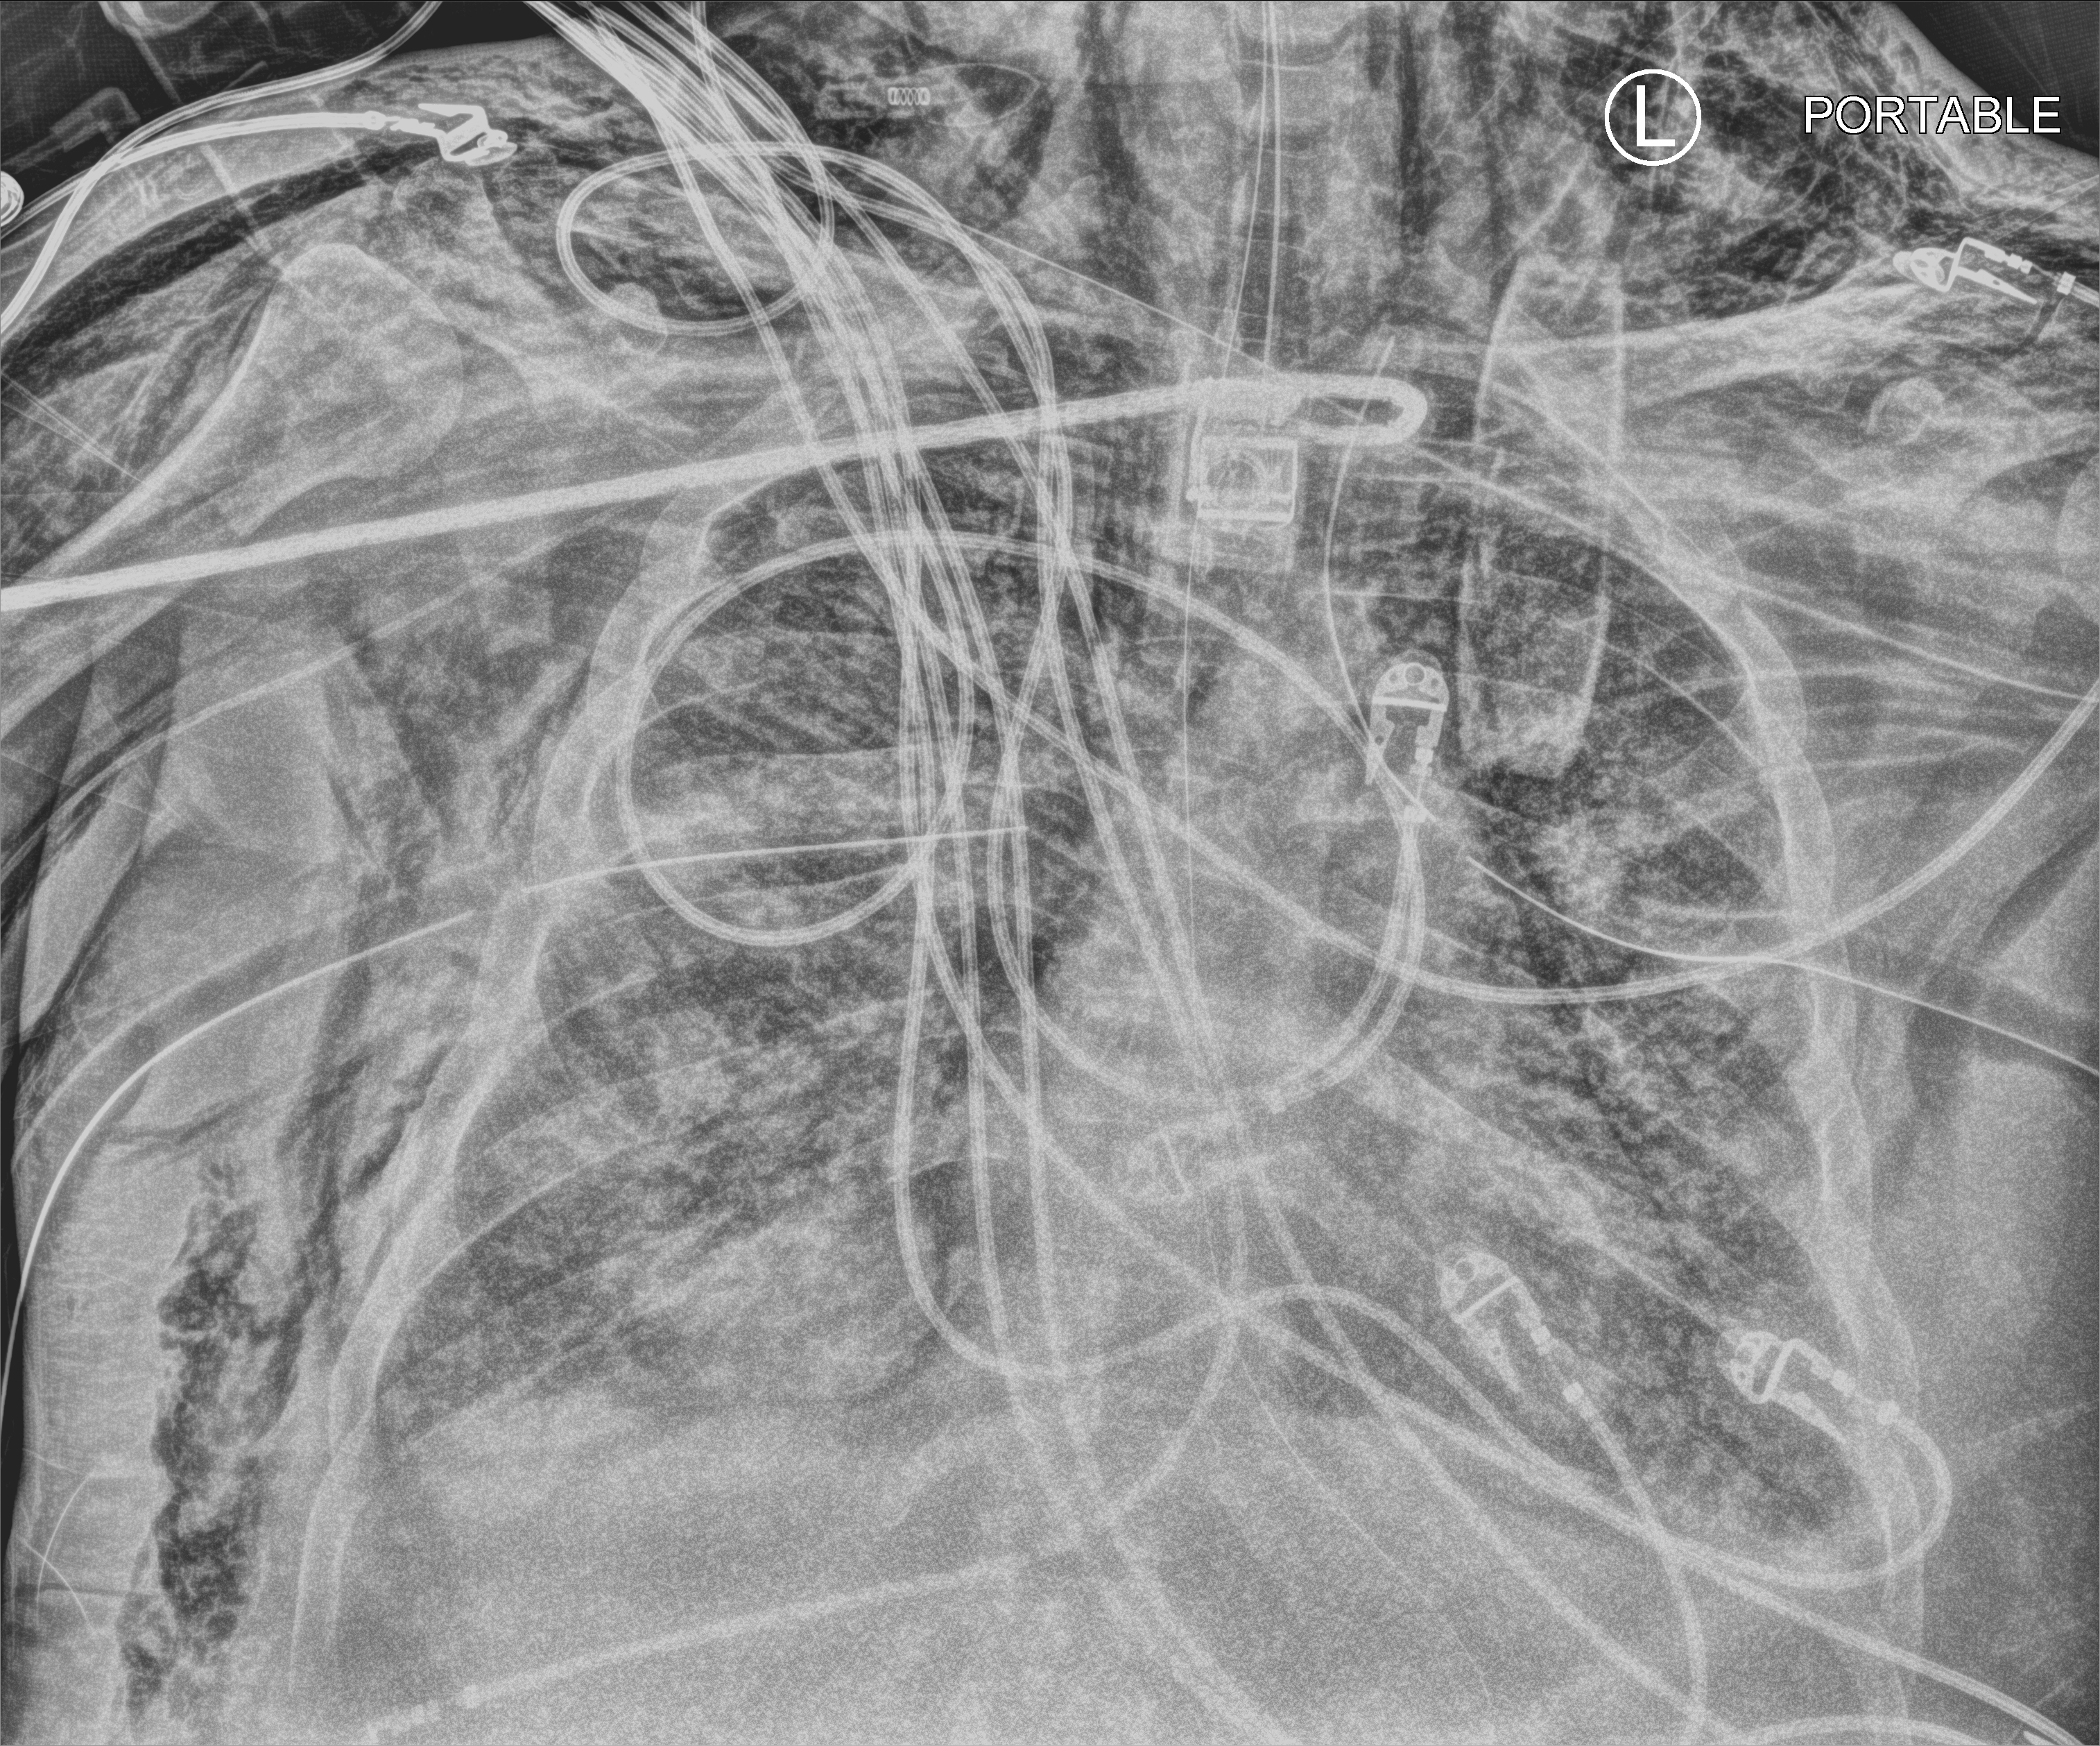
Chest X-ray (portable), anteroposterior (AP) projection. Adult patient hospitalised with COVID-19, age 18–59 years.
Admission-level facts for this patient (not findings on this image; timing relative to this image not recorded):
- admitted to intensive care during this hospital stay: yes